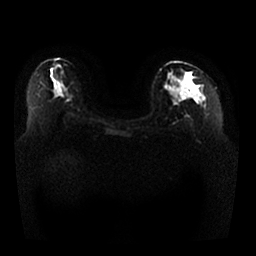
Breast MRI, one axial slice; slice 16 of 25 in the series (ordered by position); diffusion-weighted series; image 2 of 4 stored at this slice position (different b-values; order by instance number); 1.5 T; 256 × 256 image matrix. Female patient.
Structures marked on this image (manually delineated by an expert):
- tumour on diffusion-weighted imaging: bounding box [x1, y1, x2, y2] px = [178, 85, 196, 98]